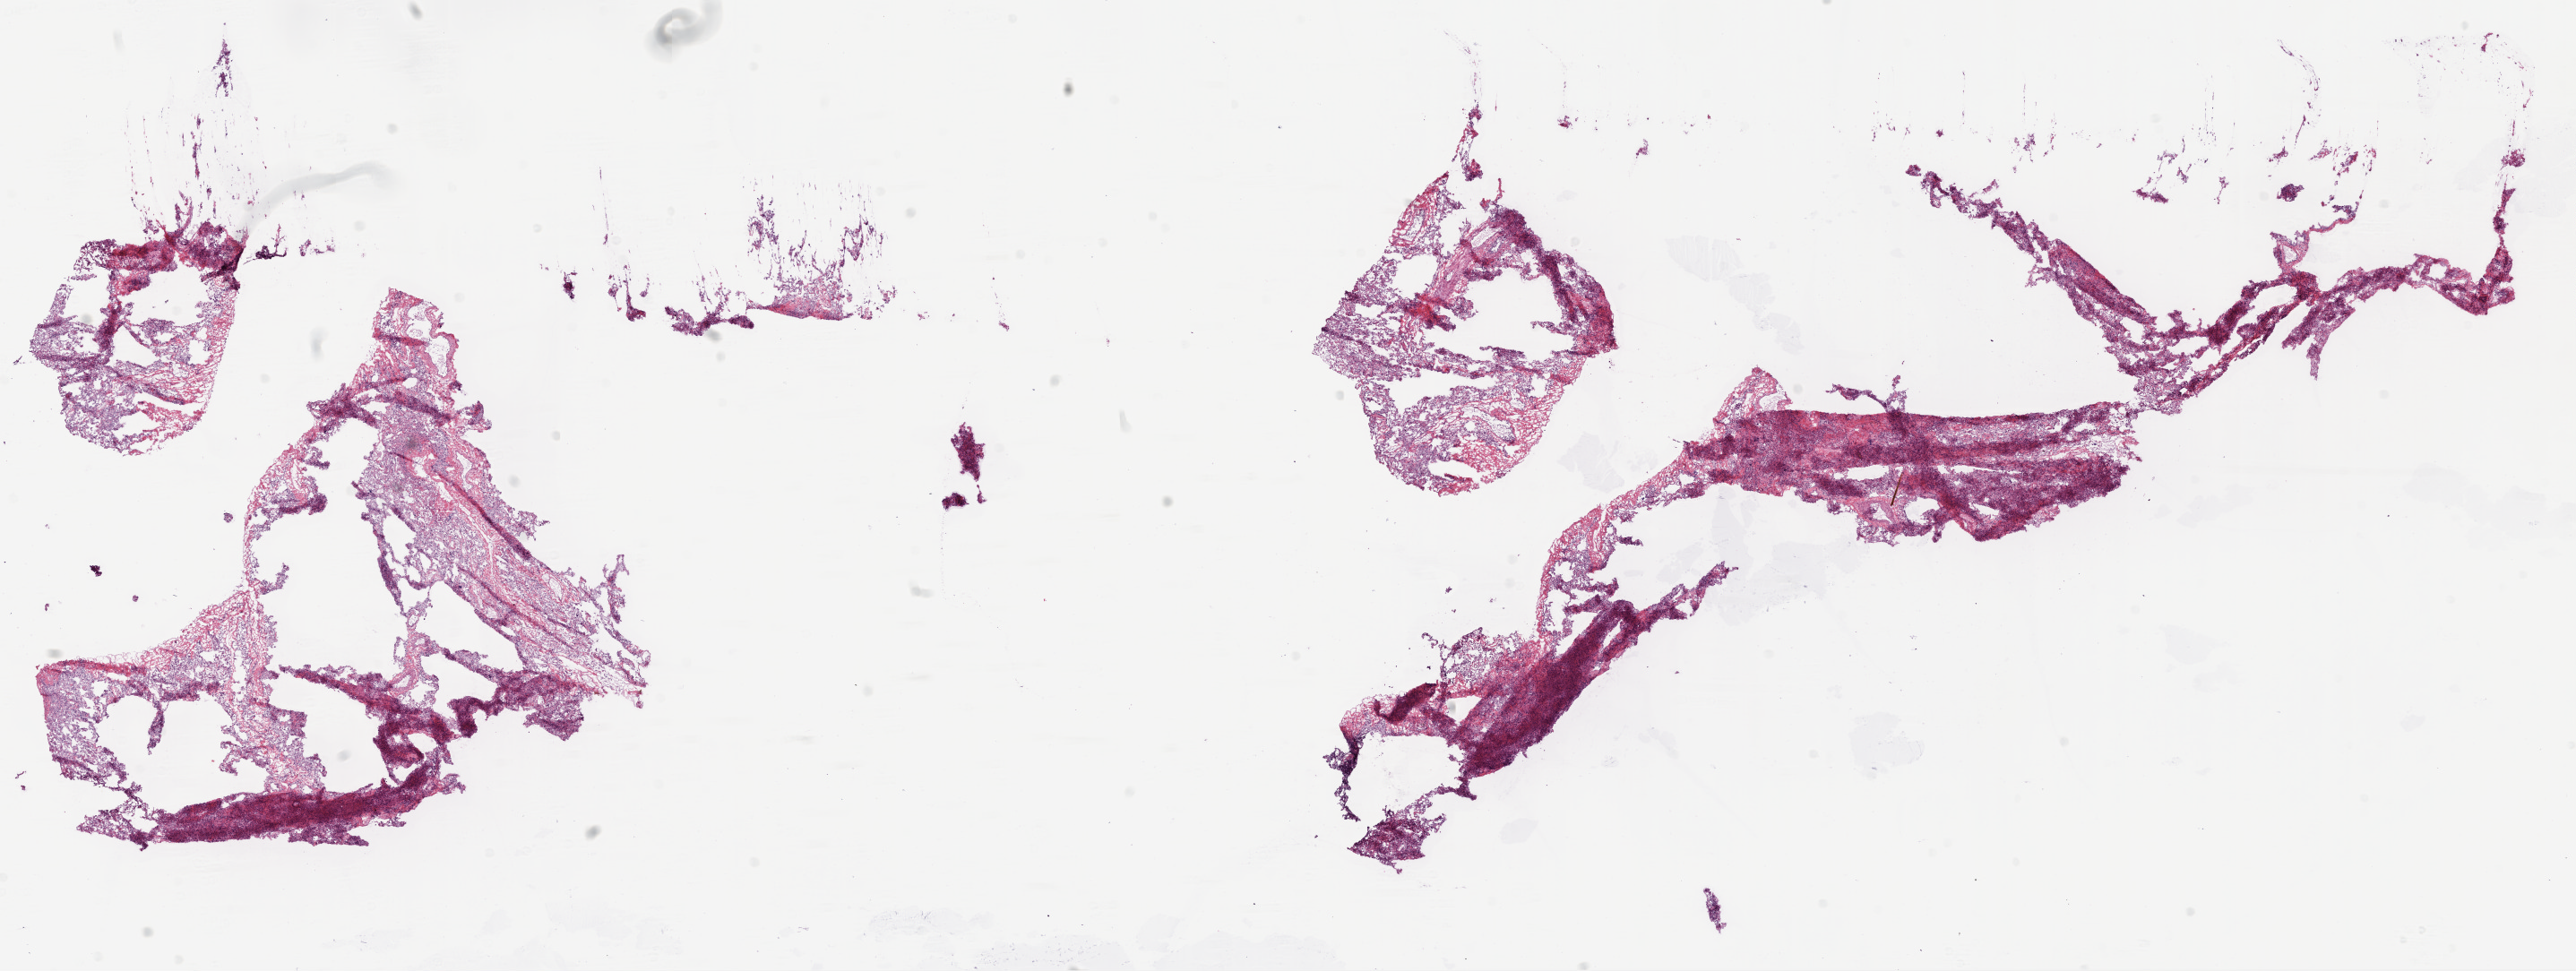
Digitized H&E tissue section (whole slide), a low-resolution overview of the entire scanned area, about 23.1 x 8.7 mm (slide scanned at 20x). Frozen section. Solid tissue normal (non-tumour tissue) sample from the lung. Female patient; age at initial diagnosis 65 years.
This section: solid tissue normal sample (biorepository sample class). Patient diagnosis: Squamous cell carcinoma, NOS.